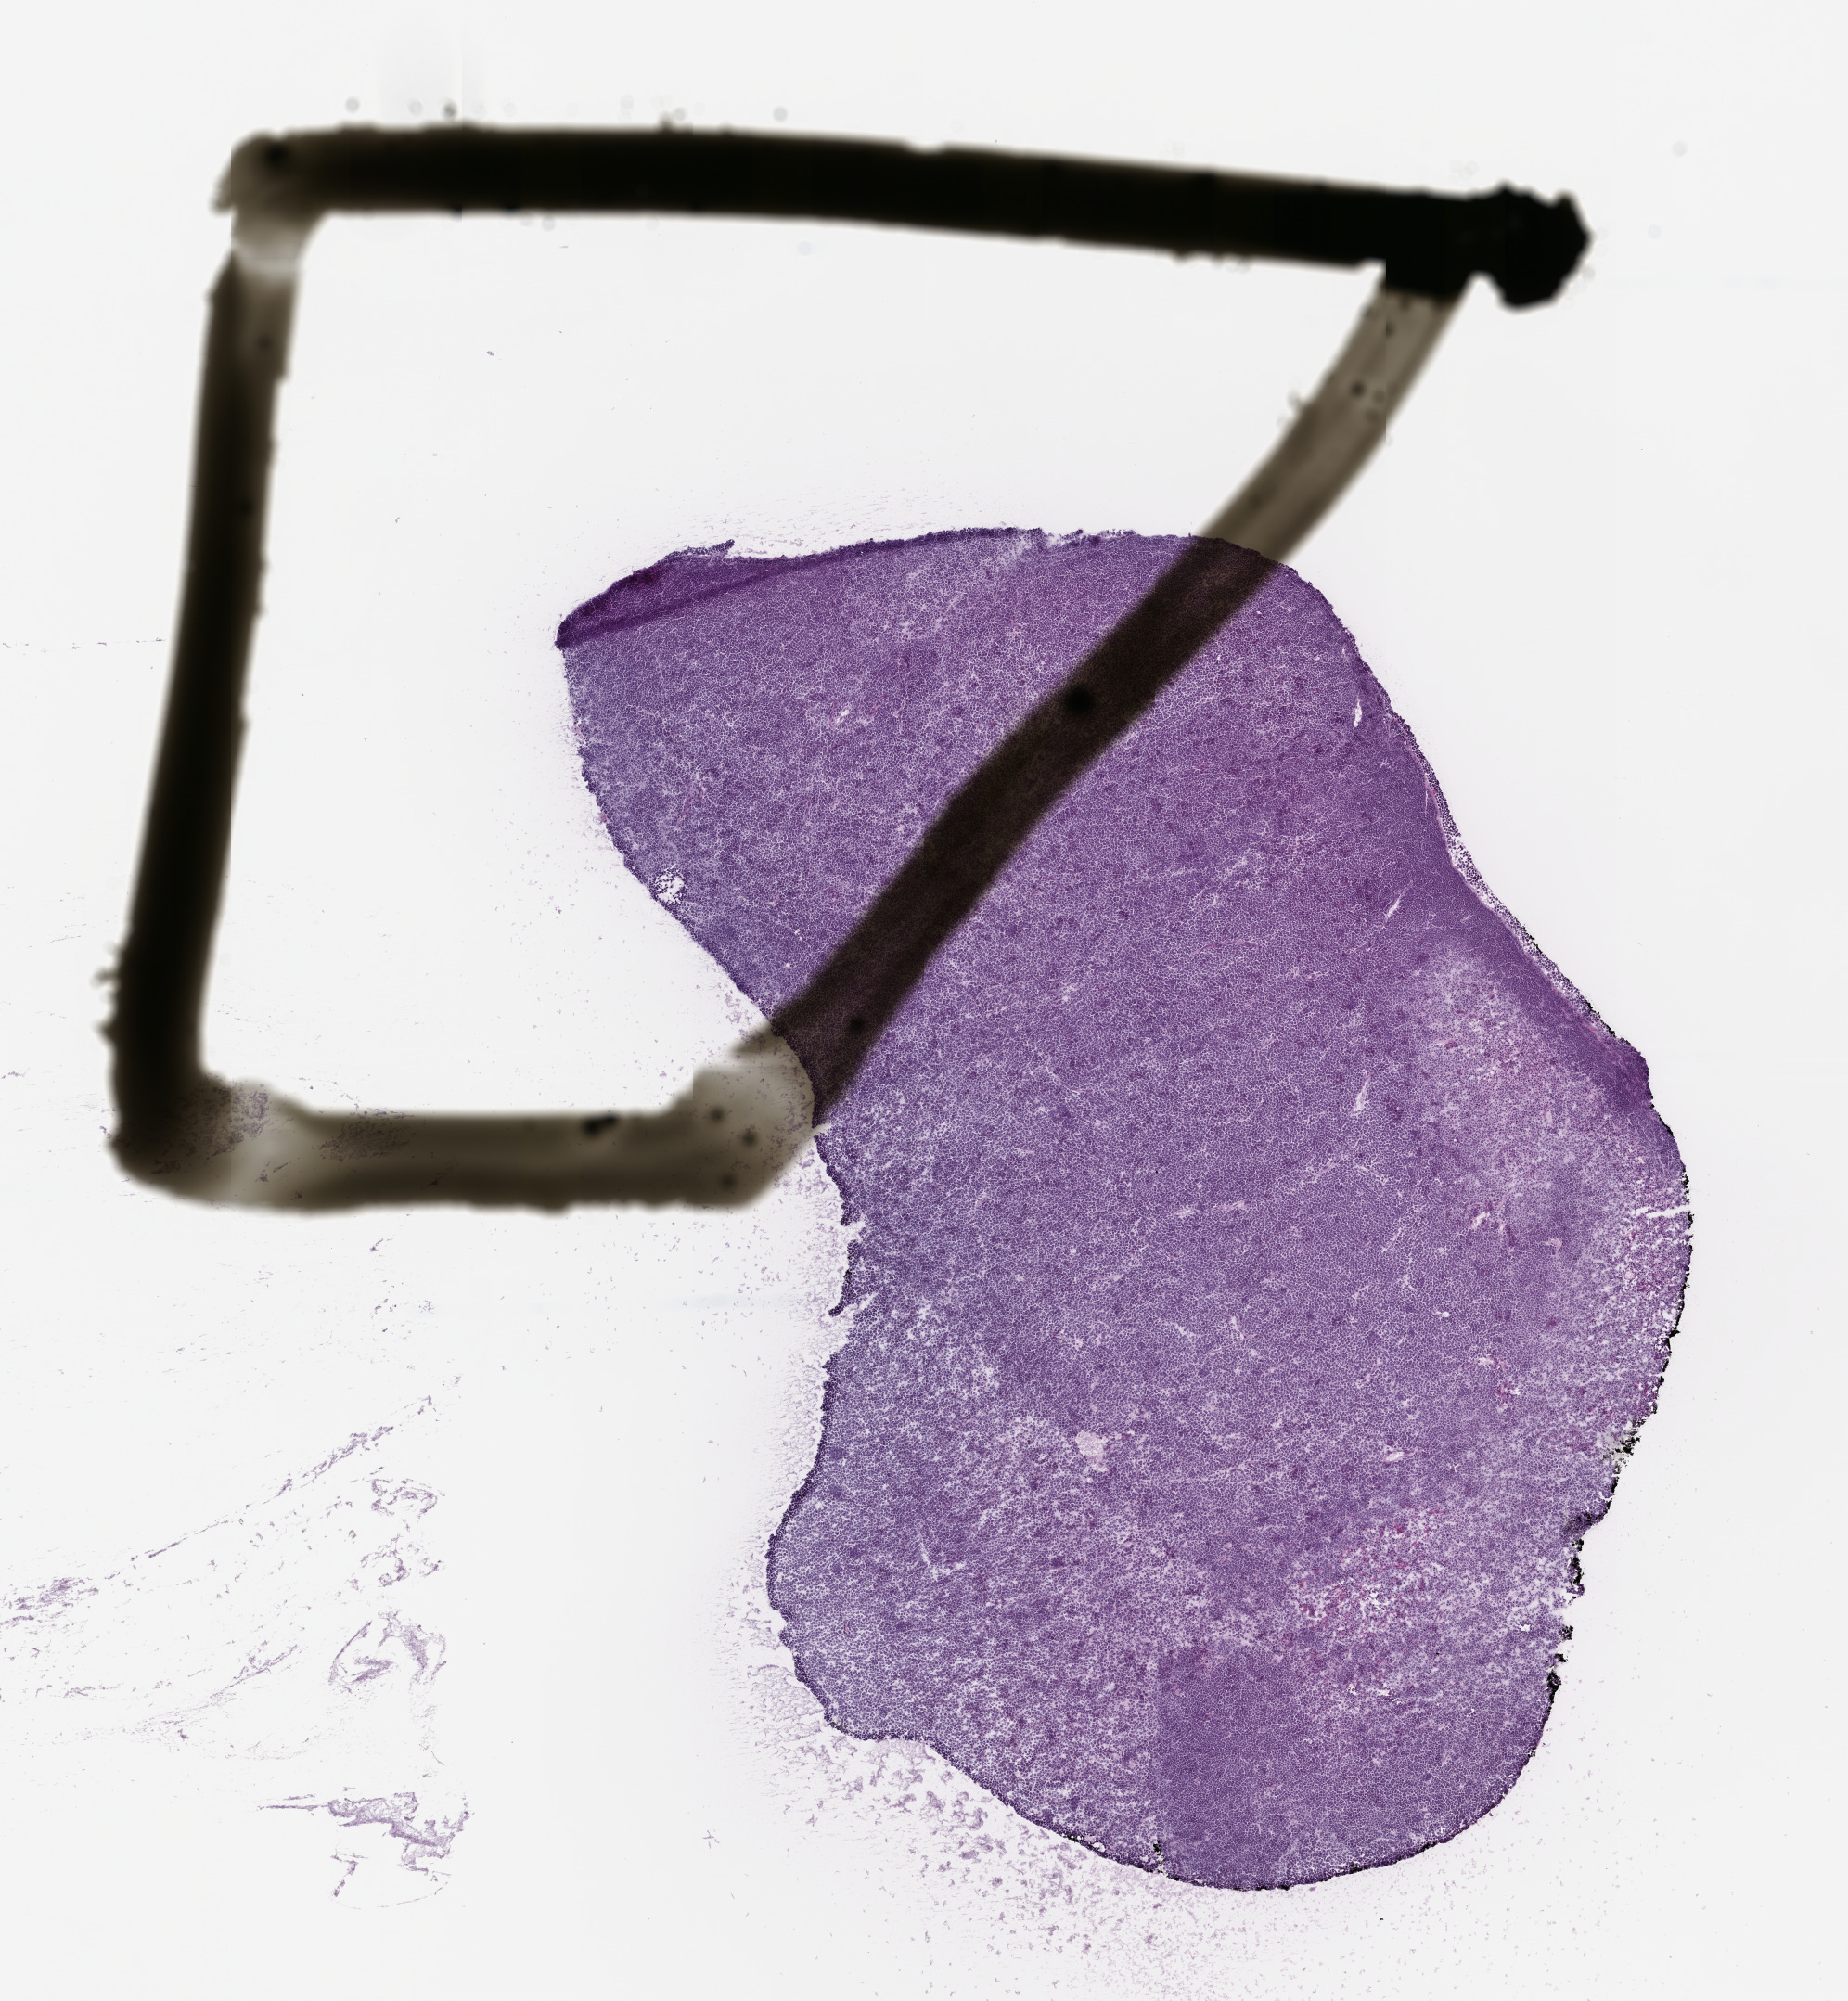
Hematoxylin and eosin (H&E) whole-slide image of a patient-derived xenograft (PDX) tumor grown in a mouse, passage 0 — a low-resolution overview of the entire scanned area, about 8.0 x 8.7 mm. FFPE section. Originating tumor site category: endocrine.
Originating patient diagnosis: Merkel Cell Carcinoma.